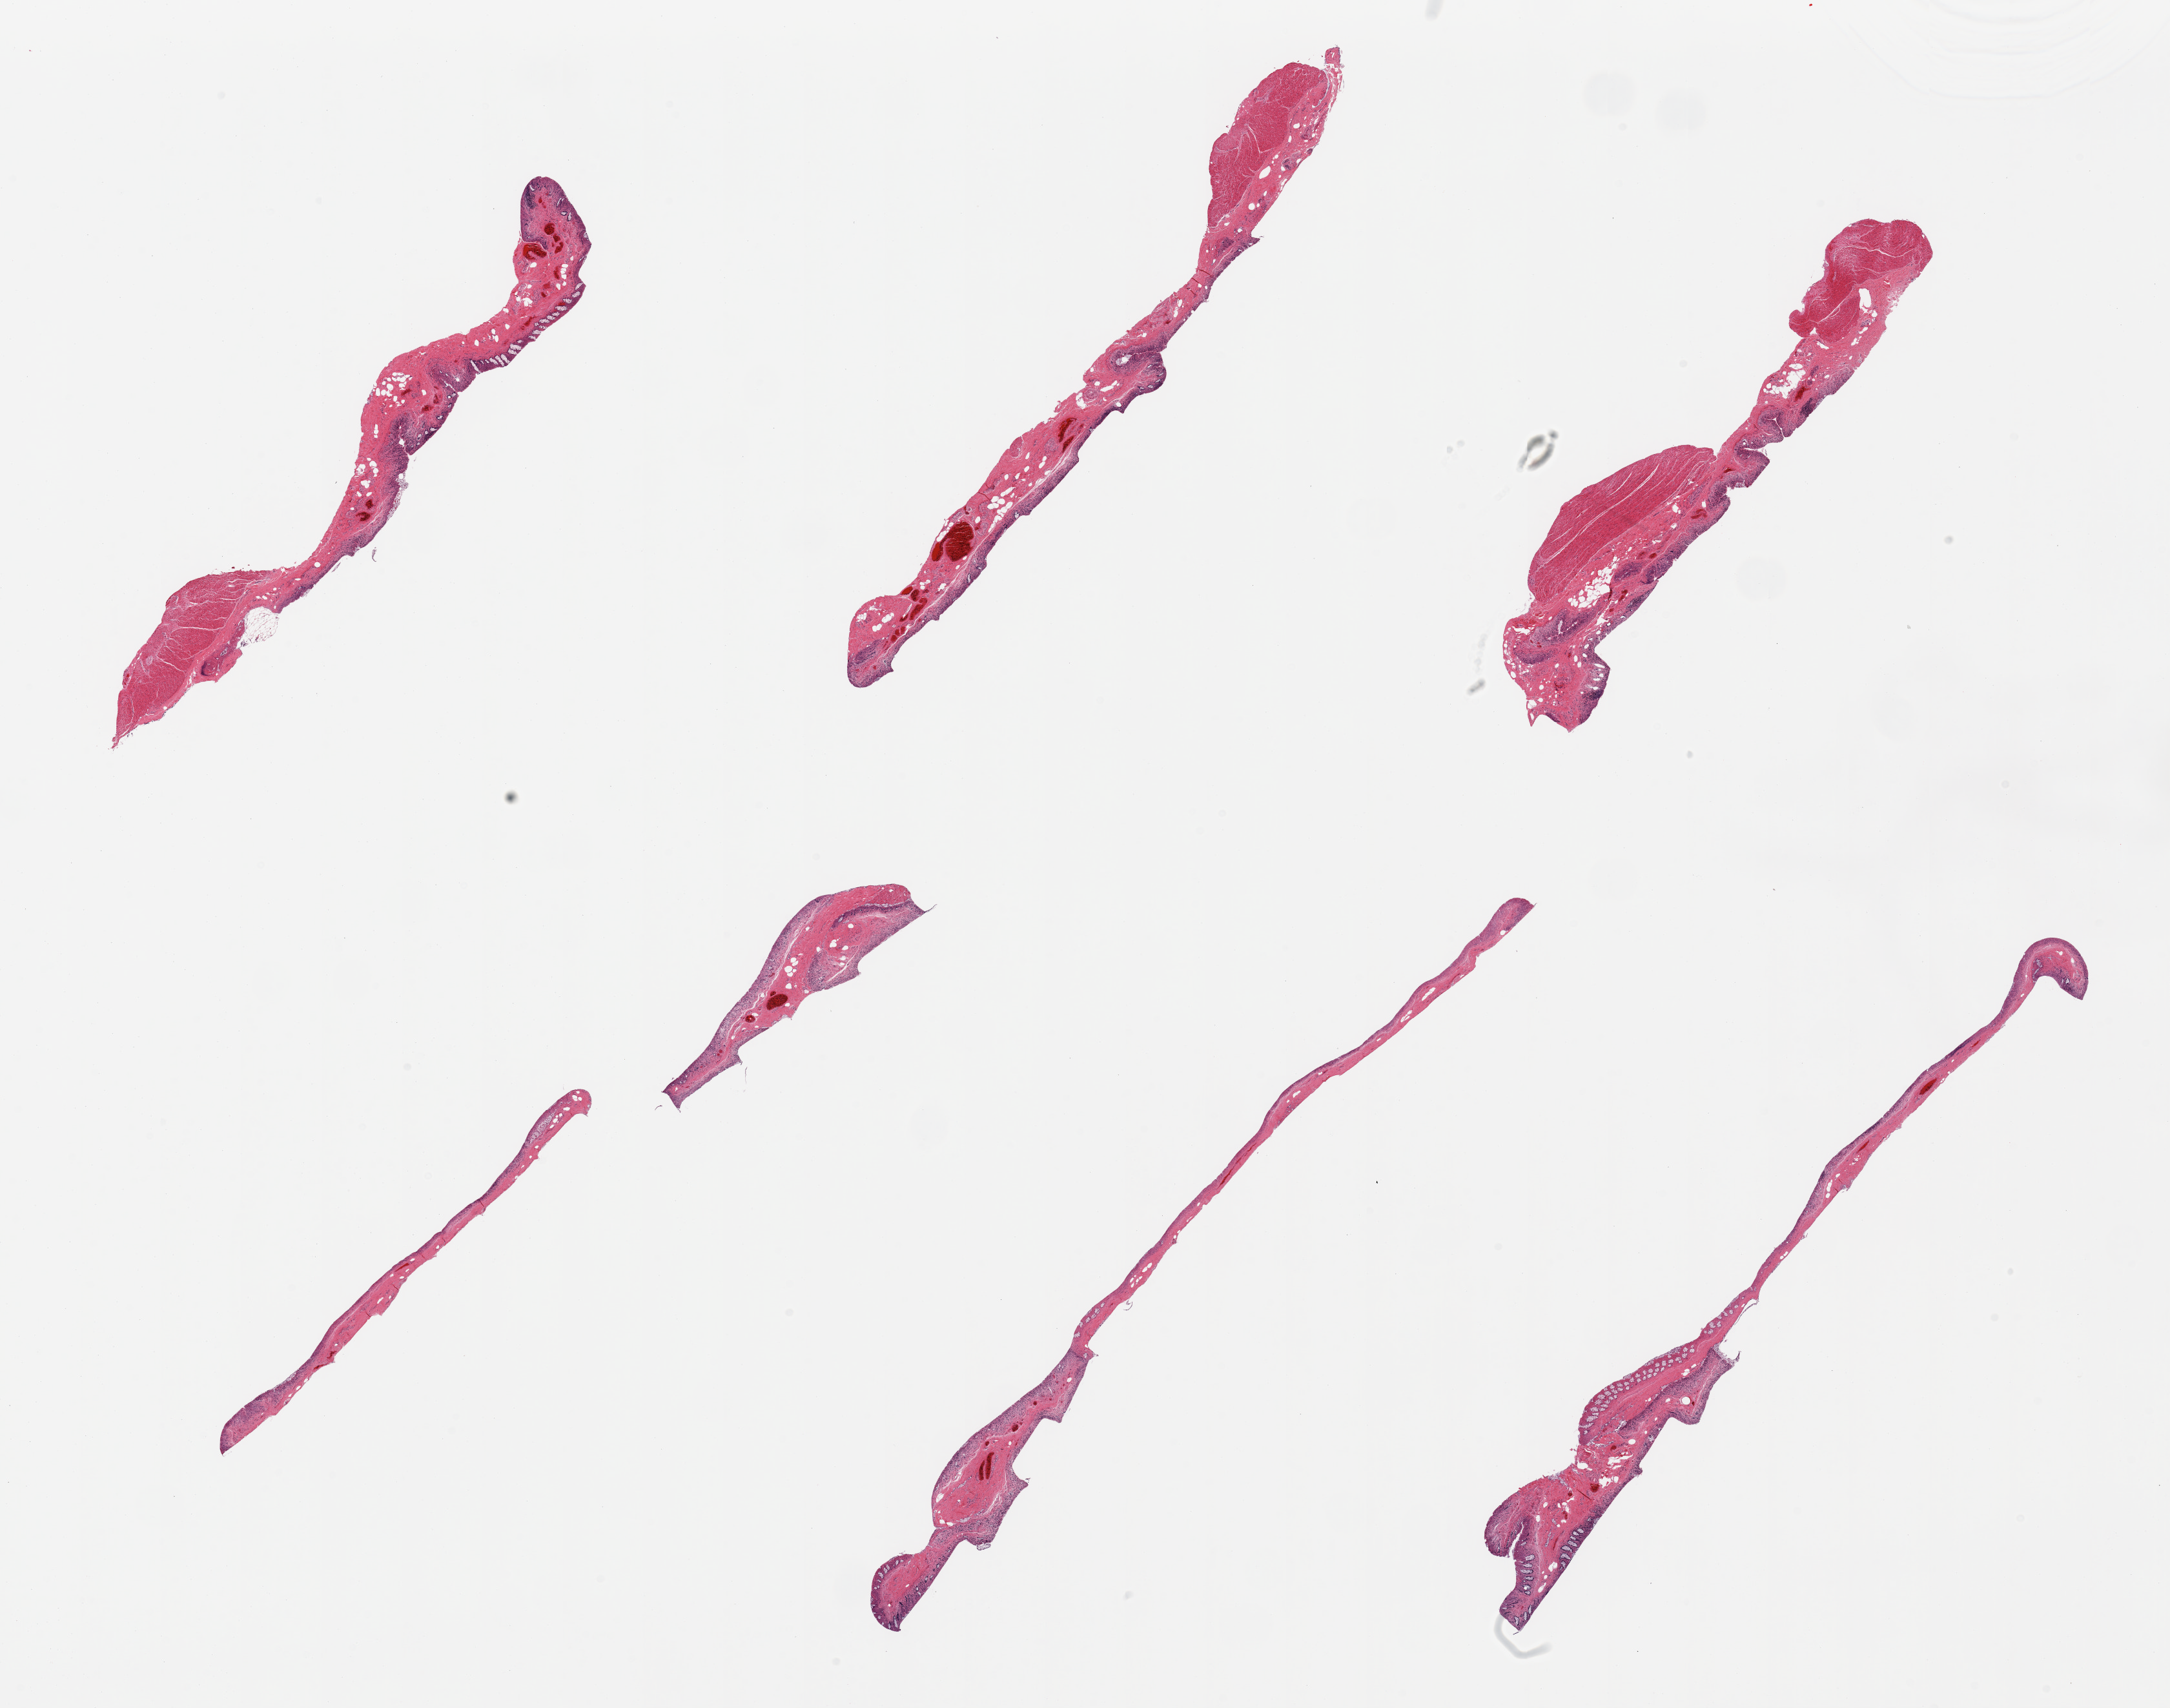
Hematoxylin and eosin (H&E) whole-slide image — whole scanned area (about 26.6 x 20.9 mm) shown as a low-resolution overview. PAXgene-fixed, paraffin-embedded tissue. Target tissue: transverse colon. Donor tissue sample. Female donor.
Pathologist's review note for this sample: 6 pieces, totally autolyzed/sloughed mucosa.